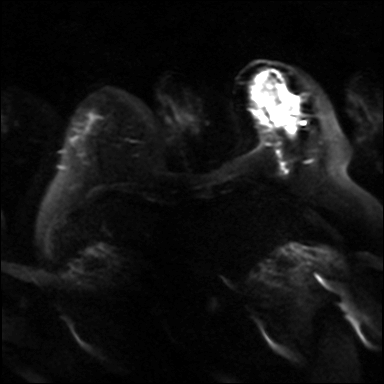
Breast MRI, one axial slice. Slice 7 of 36 in the series (ordered by position). Diffusion-weighted series; image 2 of 4 stored at this slice position (different b-values; order by instance number). 3 T. 4 mm slice thickness. 384 × 384 image matrix, field of view 320 × 320 mm. Female patient.
Annotated regions visible in this slice (outlined manually by an expert reader):
- tumour on diffusion-weighted imaging: bounding box <285,114,295,126> (left, top, right, bottom; pixels)